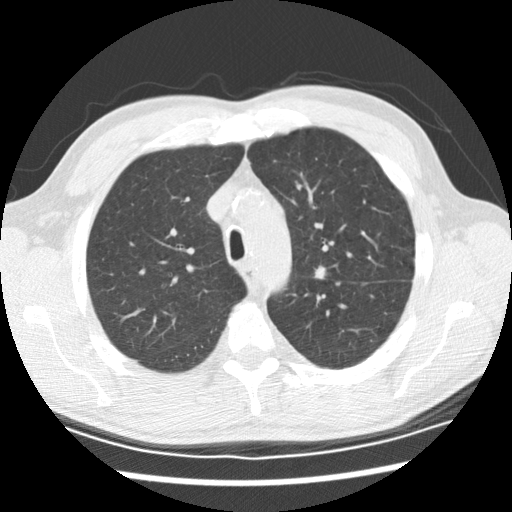
Chest CT (low-dose screening protocol), one axial image; second screening round (one year after baseline); lung window (W 1500 / L -600 HU); standard (soft-tissue) reconstruction kernel (STANDARD); 120 kVp; slice 56 of 208 in the series; 512 × 512 image matrix, field of view 340 × 340 mm. Male participant, aged 59 years at enrolment.
Expert reader's lesion annotation, bounding box <303,261,339,293> (left, top, right, bottom; pixels). Screening reader's record for this exam (one nodule recorded; not confirmed to be the boxed lesion): non-calcified nodule or mass ≥4 mm, left upper lobe, 8 × 7 mm, spiculated (stellate) margins, soft tissue attenuation, pre-existing on the prior screen: yes; interval growth: yes. Official screen result: positive, change unspecified: nodule(s) >= 4 mm or enlarging nodule(s), mass(es), or other non-specific abnormalities suspicious for lung cancer.